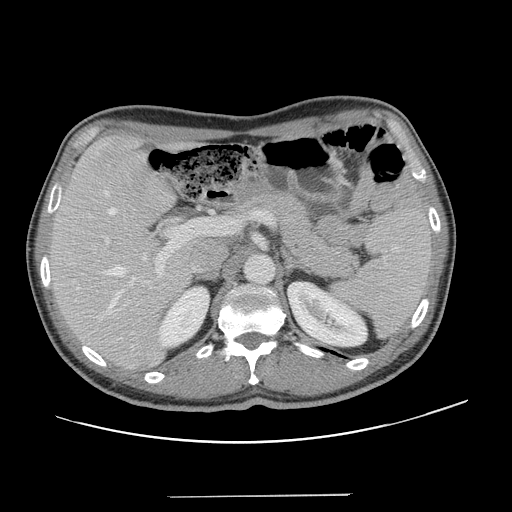
Contrast-enhanced abdominal CT, one axial slice; position 84 of 131 along the scan axis; intravenous contrast given; soft-tissue window (W 400 / L 40 HU); 512 × 512 image matrix, field of view 403 × 403 mm. Male patient, age 60 years. Case-level facts recorded for this patient, not image findings: diagnosis: colorectal cancer liver metastases, imaged before liver resection; multiple liver metastases: no; largest metastasis: 2.5 cm; disease in both lobes: no.
Outlined on this slice (outlined manually by an expert reader):
- hepatic veins: bounding box <104,191,146,314> (left, top, right, bottom; pixels)
- liver: <50,136,190,367>
- planned liver remnant (the part of the liver to remain after resection): <51,136,191,355>
- portal vein (with intrahepatic branches): <106,218,242,288>